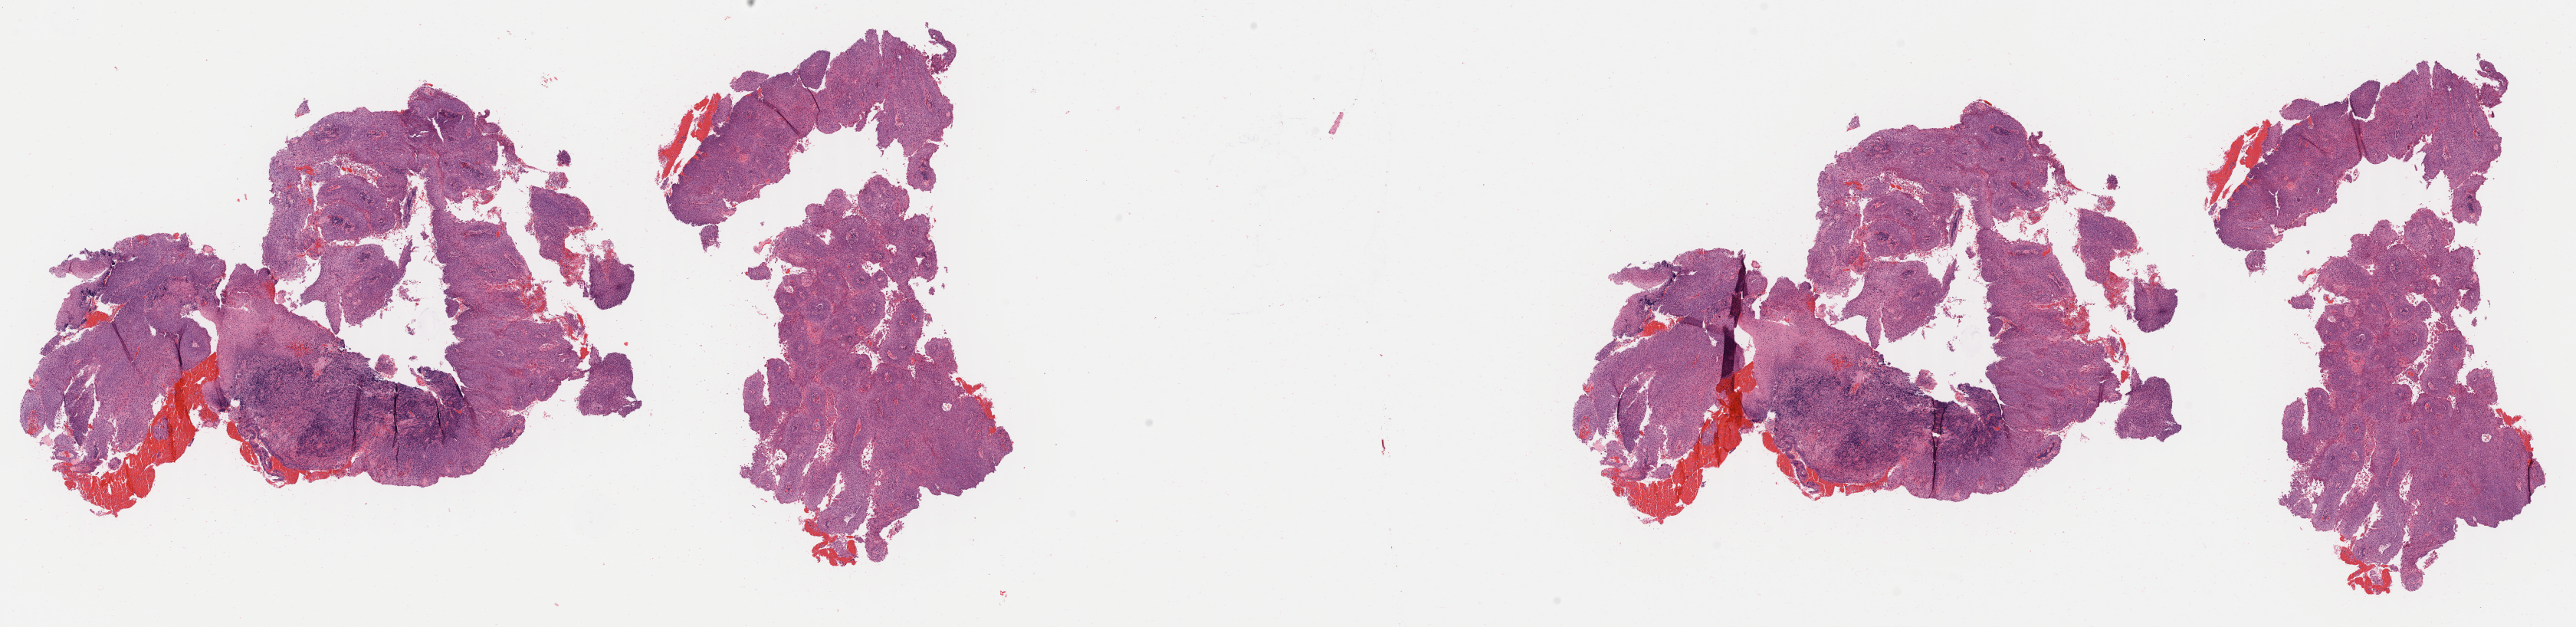
Whole-slide image, haematoxylin and eosin stain, a low-resolution overview of the entire scanned area, about 26.7 x 6.5 mm; tumor tissue; site: cervix. Patient female; aged 82.
Histologic diagnosis: Squamous cell carcinoma, keratinizing, NOS.